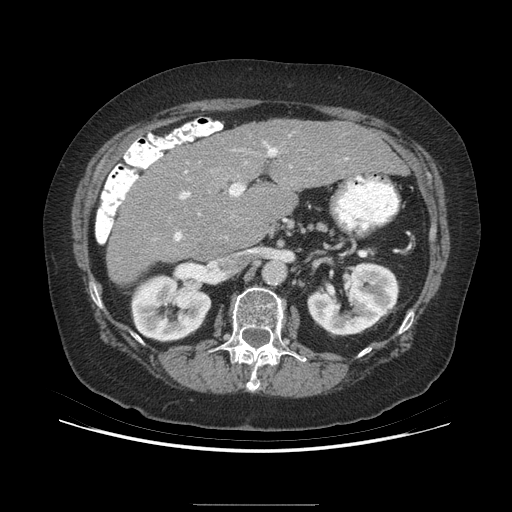
Contrast-enhanced abdominal CT (liver protocol), one axial slice. Position 149 of 192 along the scan axis. Reconstruction kernel STANDARD. 140 kVp. Soft-tissue window (W 400 / L 40 HU). 2.5 mm slice thickness. 512 × 512 image matrix. Case-level facts recorded for this patient, not image findings: diagnosis: hepatocellular carcinoma (patient treated with transarterial chemoembolisation; whether this scan precedes or follows treatment is not stated here); TNM stage (as recorded): Stage-I; Child-Pugh class: A; tumour differentiation: moderately differentiated; tumour nodularity: uninodular.
Structures marked on this image (semi-automatically segmented with operator editing):
- liver parenchyma outside the tumour (the mass and vessels are separate outlines, so this box may not span the whole liver): bounding box <106,120,405,284> (left, top, right, bottom; pixels)
- liver vessels: <174,142,278,241>